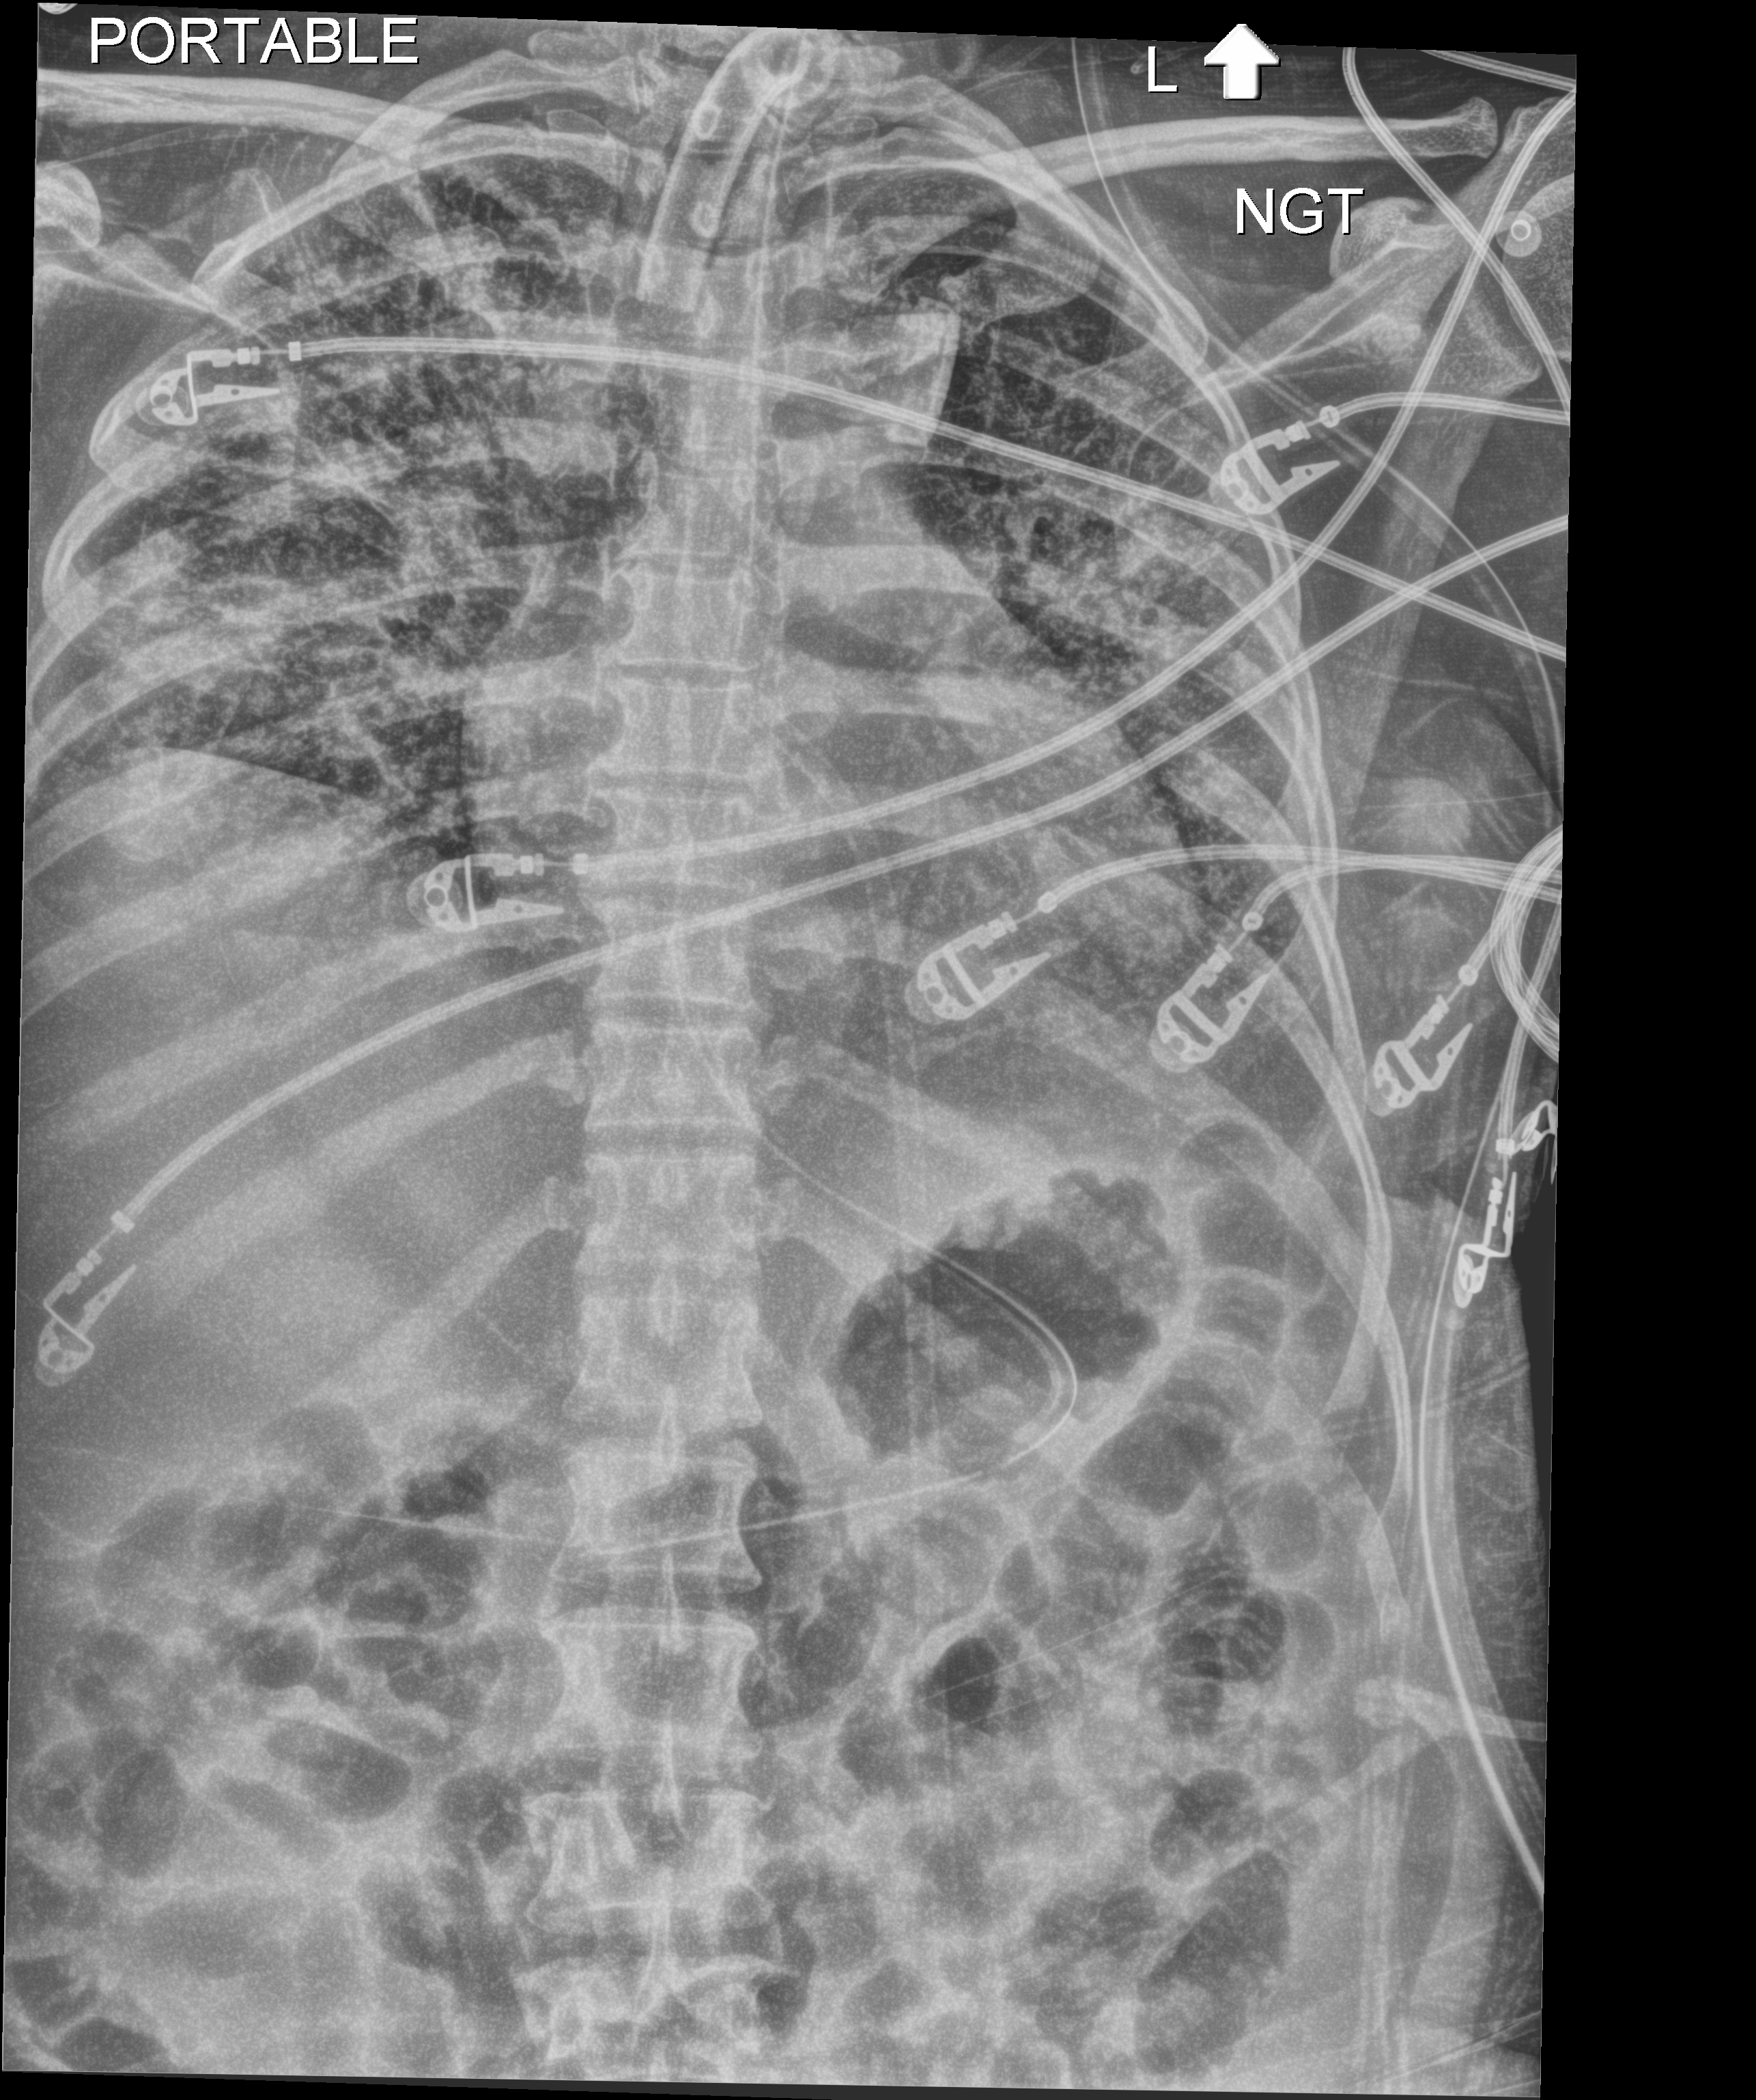
Bedside chest radiograph (digital radiography); anteroposterior (AP) projection. Patient hospitalised with COVID-19; female, aged 18–59 years.
Hospital-stay facts (about this admission, not read from this image; timing relative to this image not recorded):
- COPD (admission record): no
- length of hospital stay: 71 days